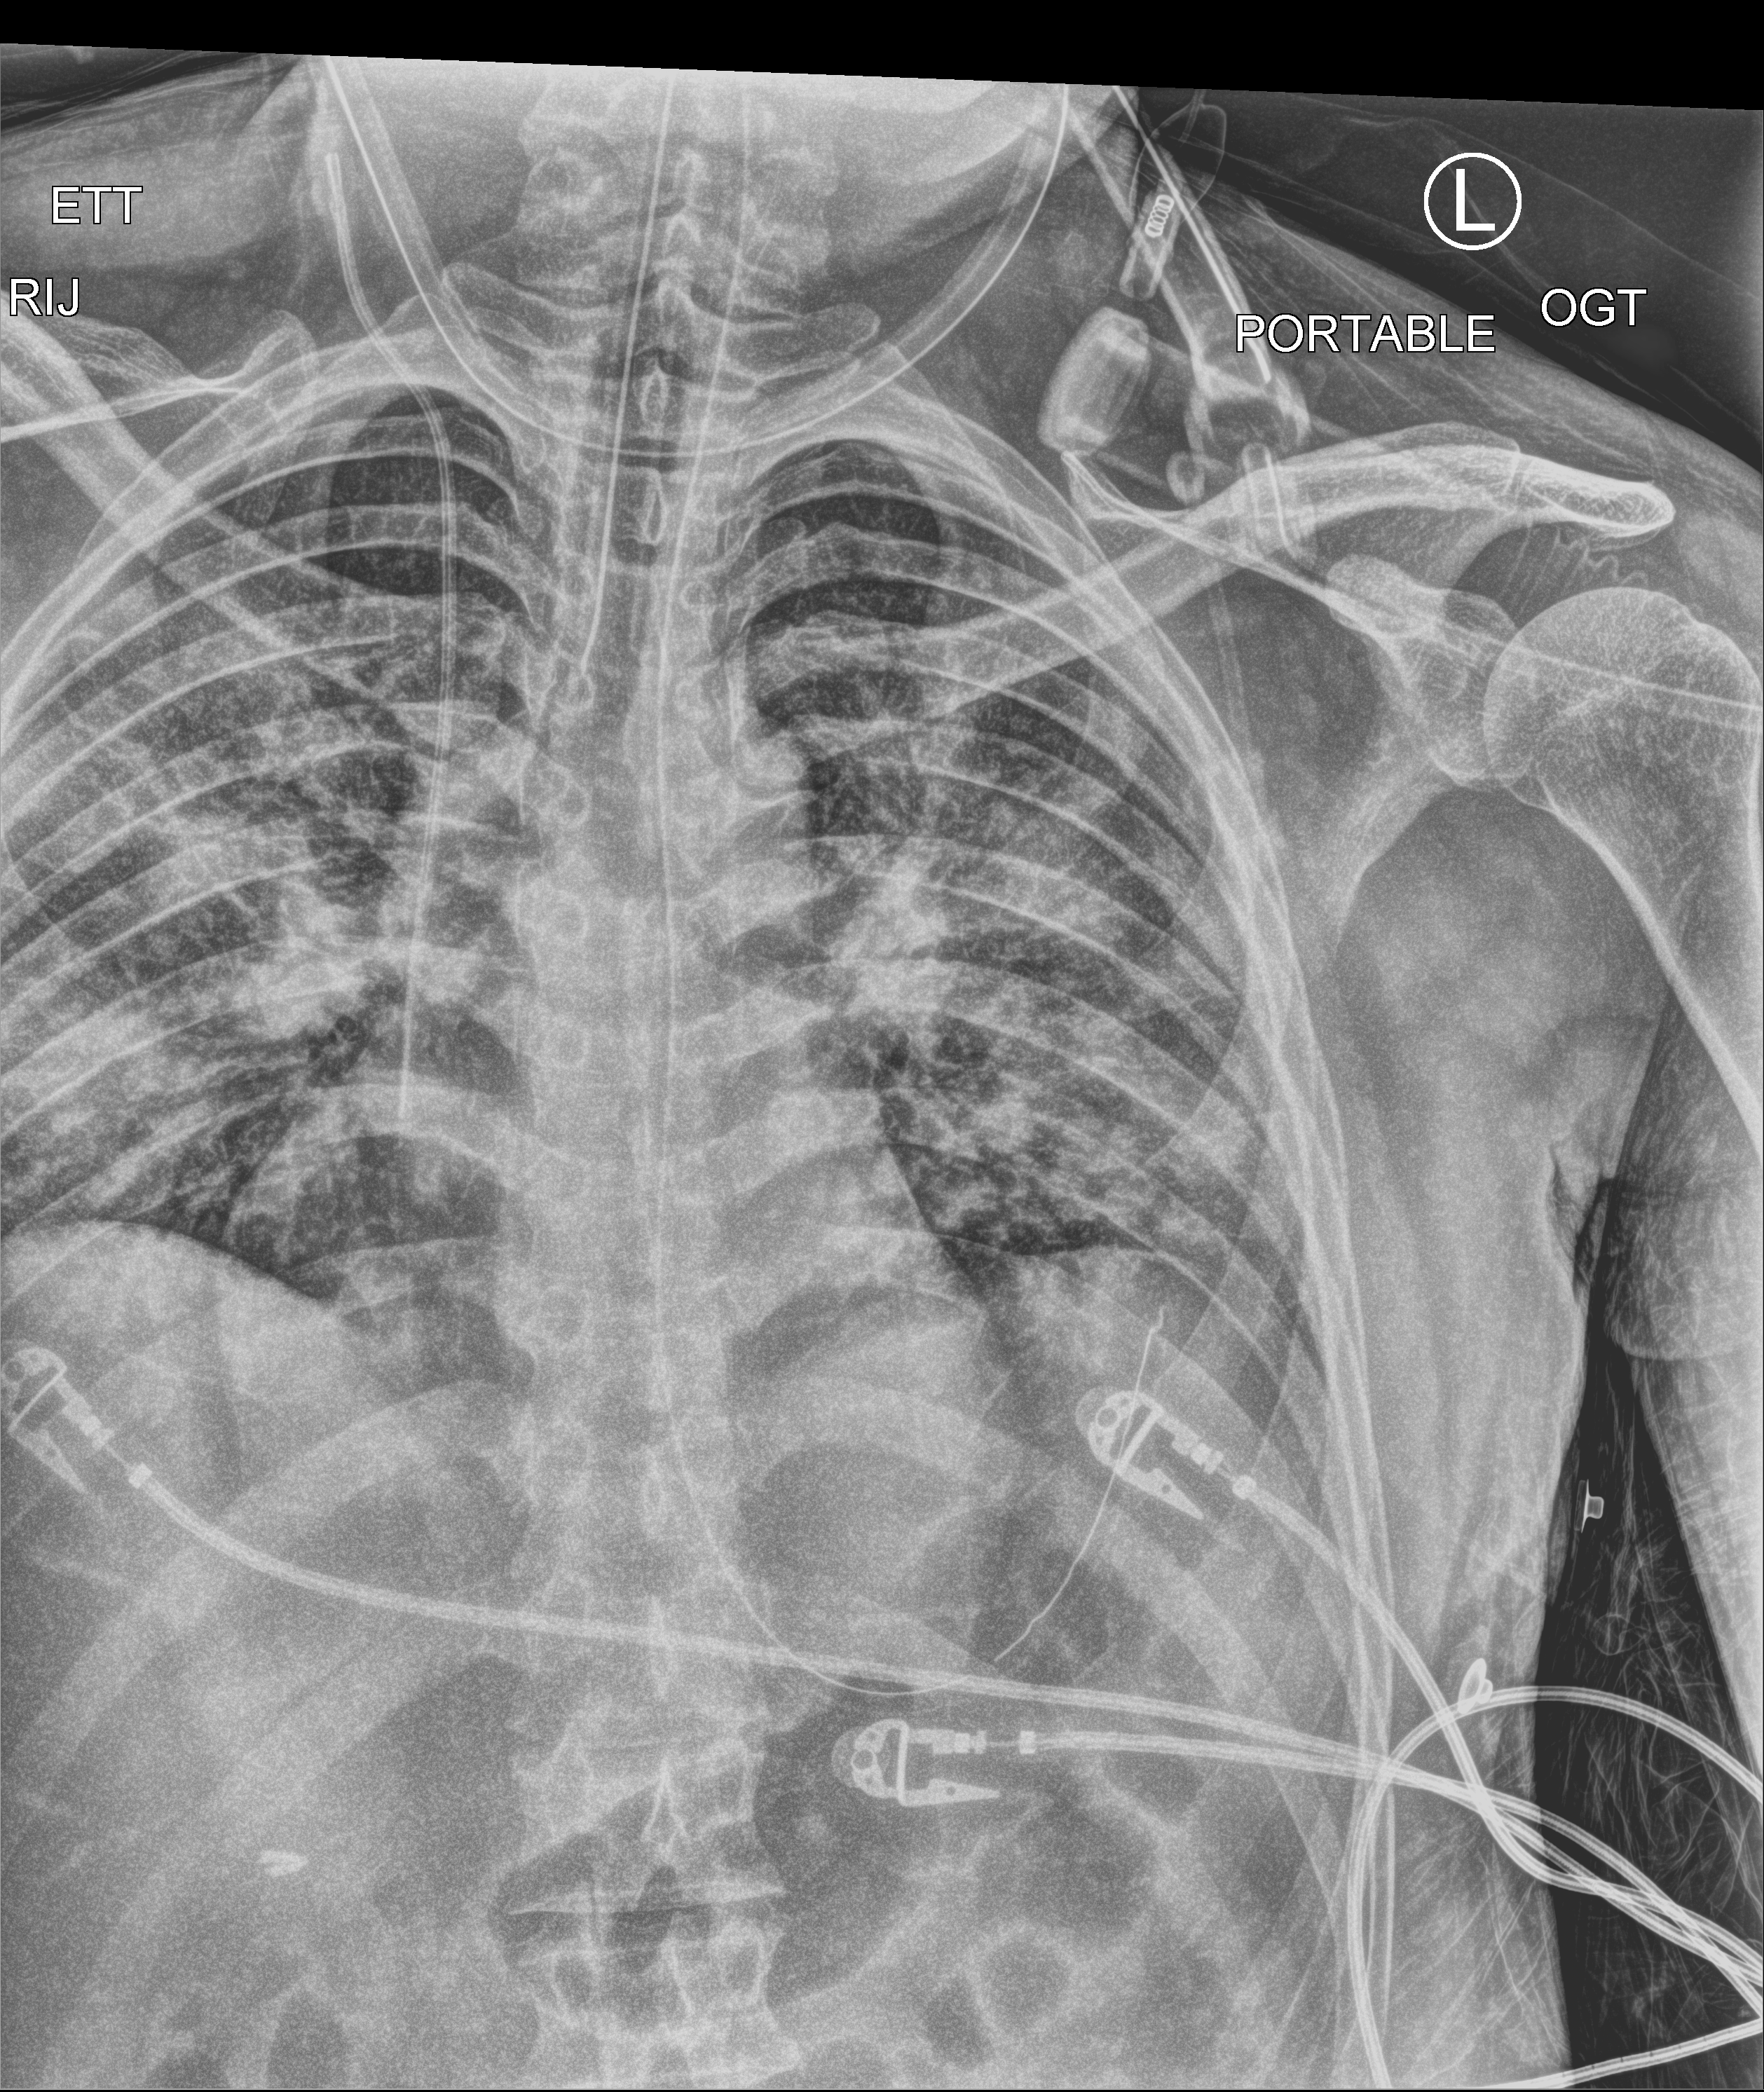
Portable chest radiograph, anteroposterior (AP) projection. Male patient hospitalised with COVID-19, age 18–59 years.
From the hospital-stay record, not from the radiograph (when in the stay this image was taken is not recorded):
- diabetes (admission record): no